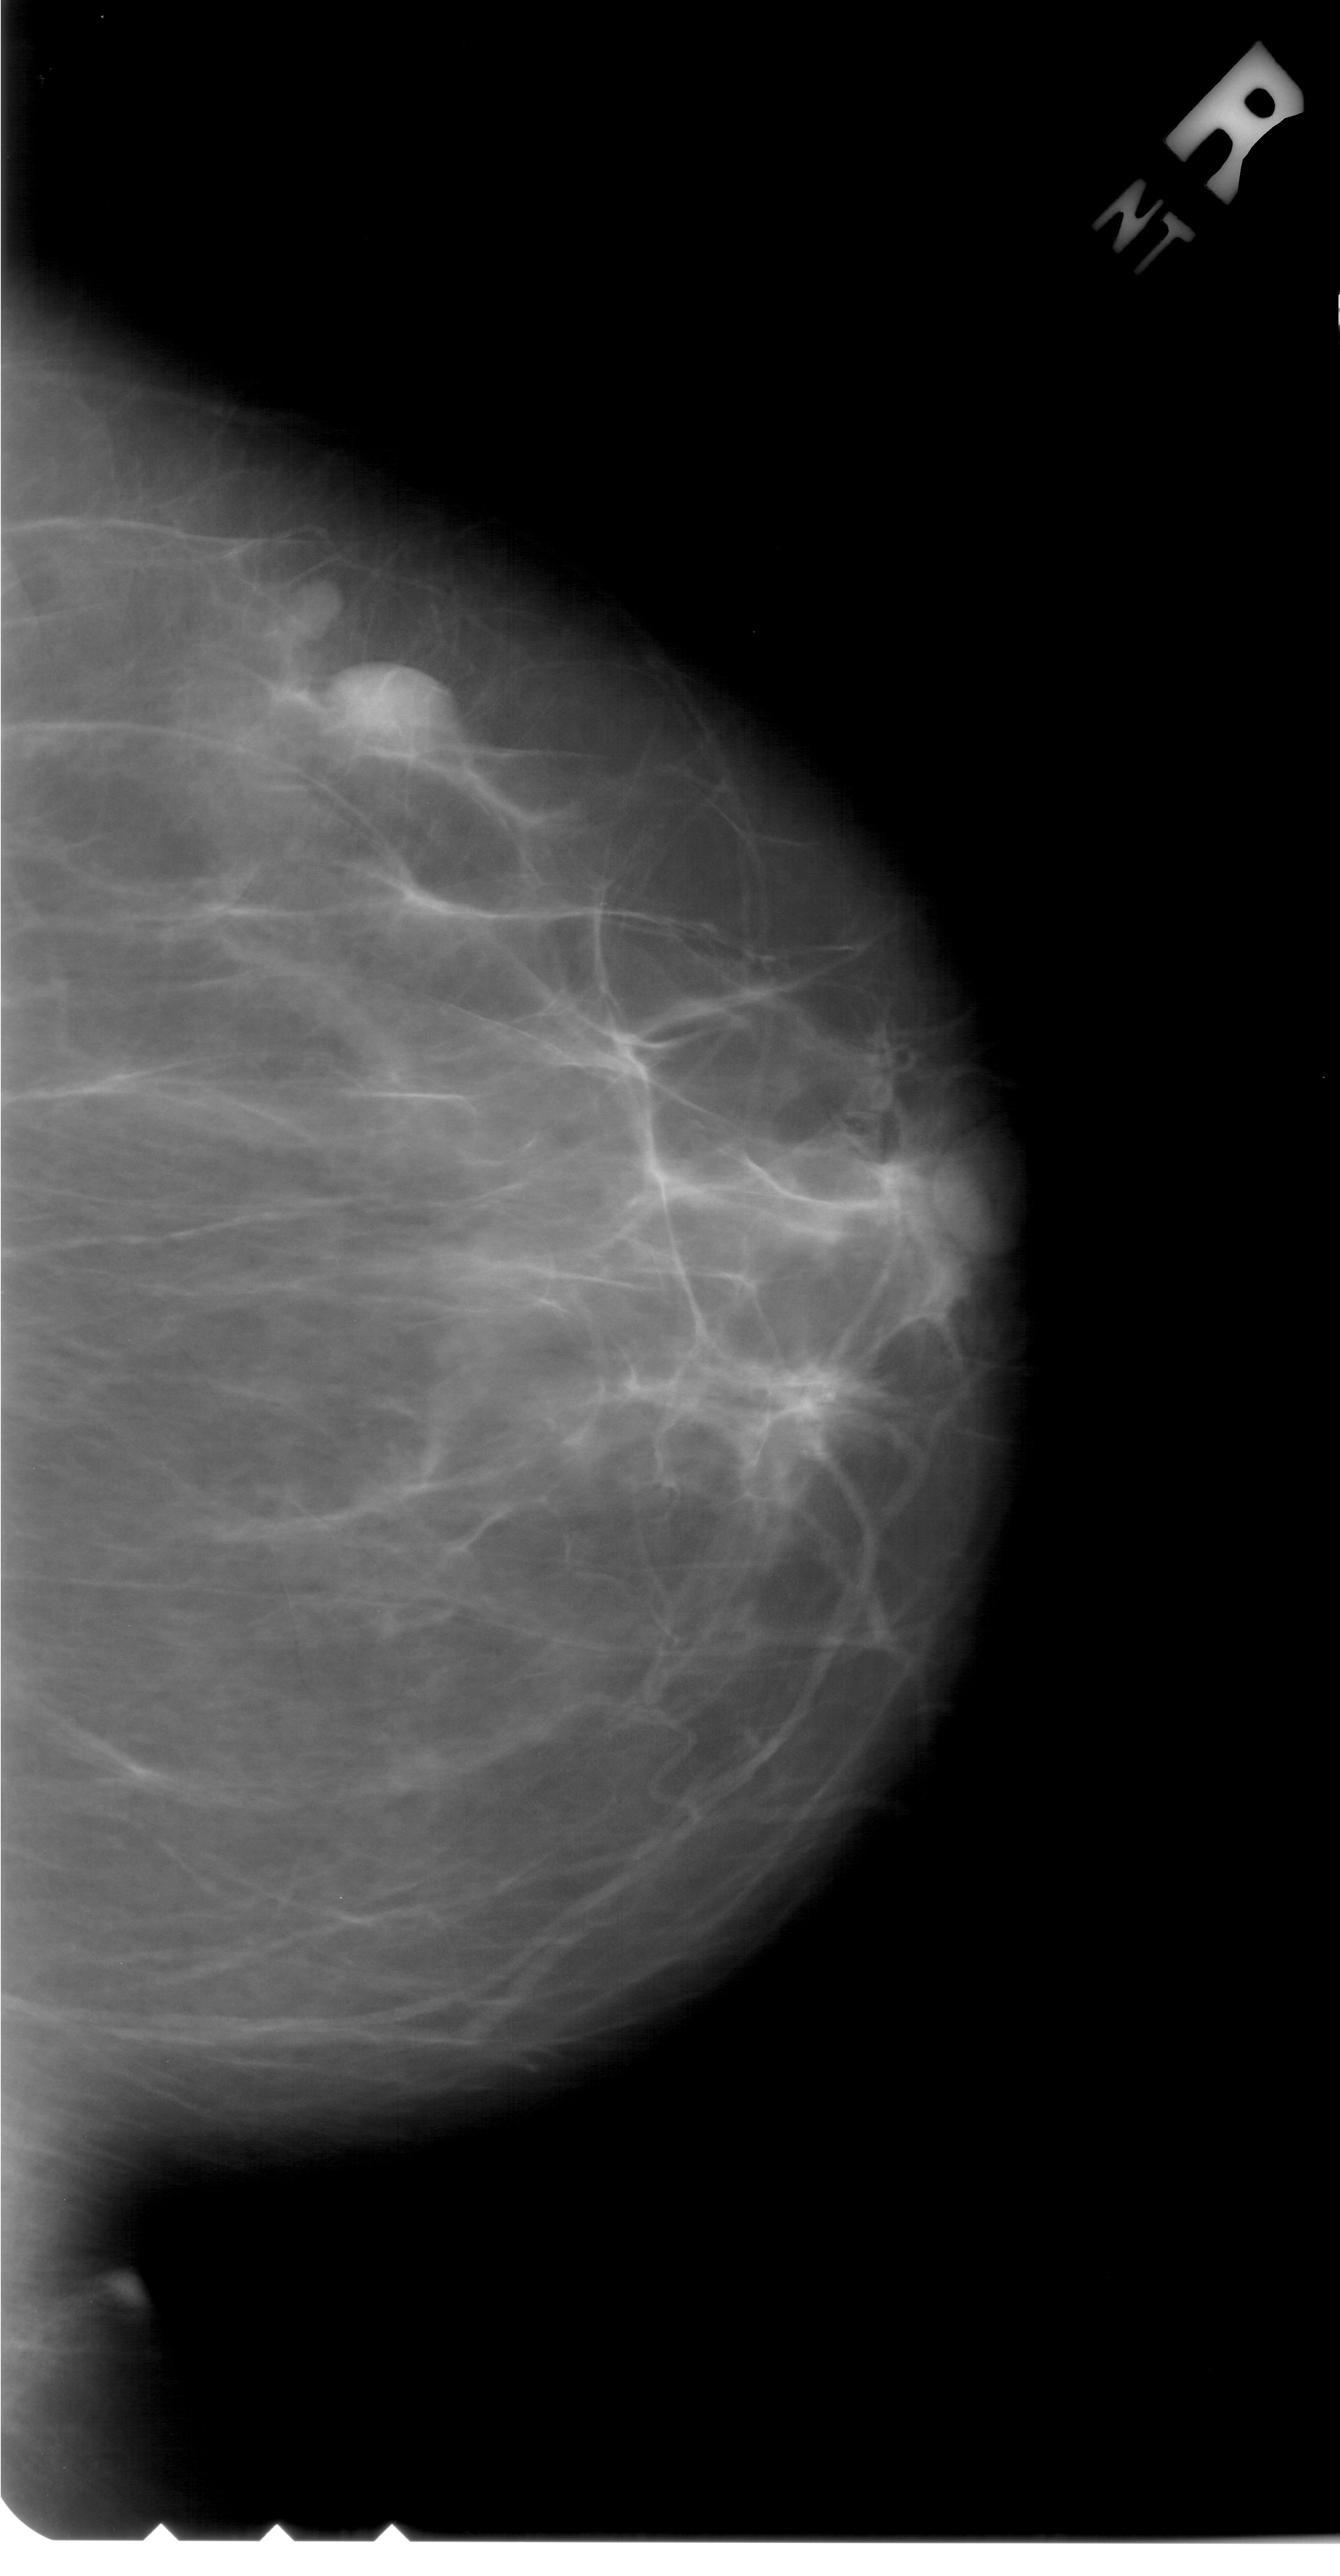
Scanned film-screen mammogram; right breast; CC view; BI-RADS breast density category 1 (scale 1–4); 1340 × 2576 image matrix.
Expert-marked regions of interest on this image (one box per marked abnormality):
- mass, shape oval, margins obscured; BI-RADS assessment category 4; pathology (as recorded): benign: box from (x=327, y=658) to (x=427, y=738) px